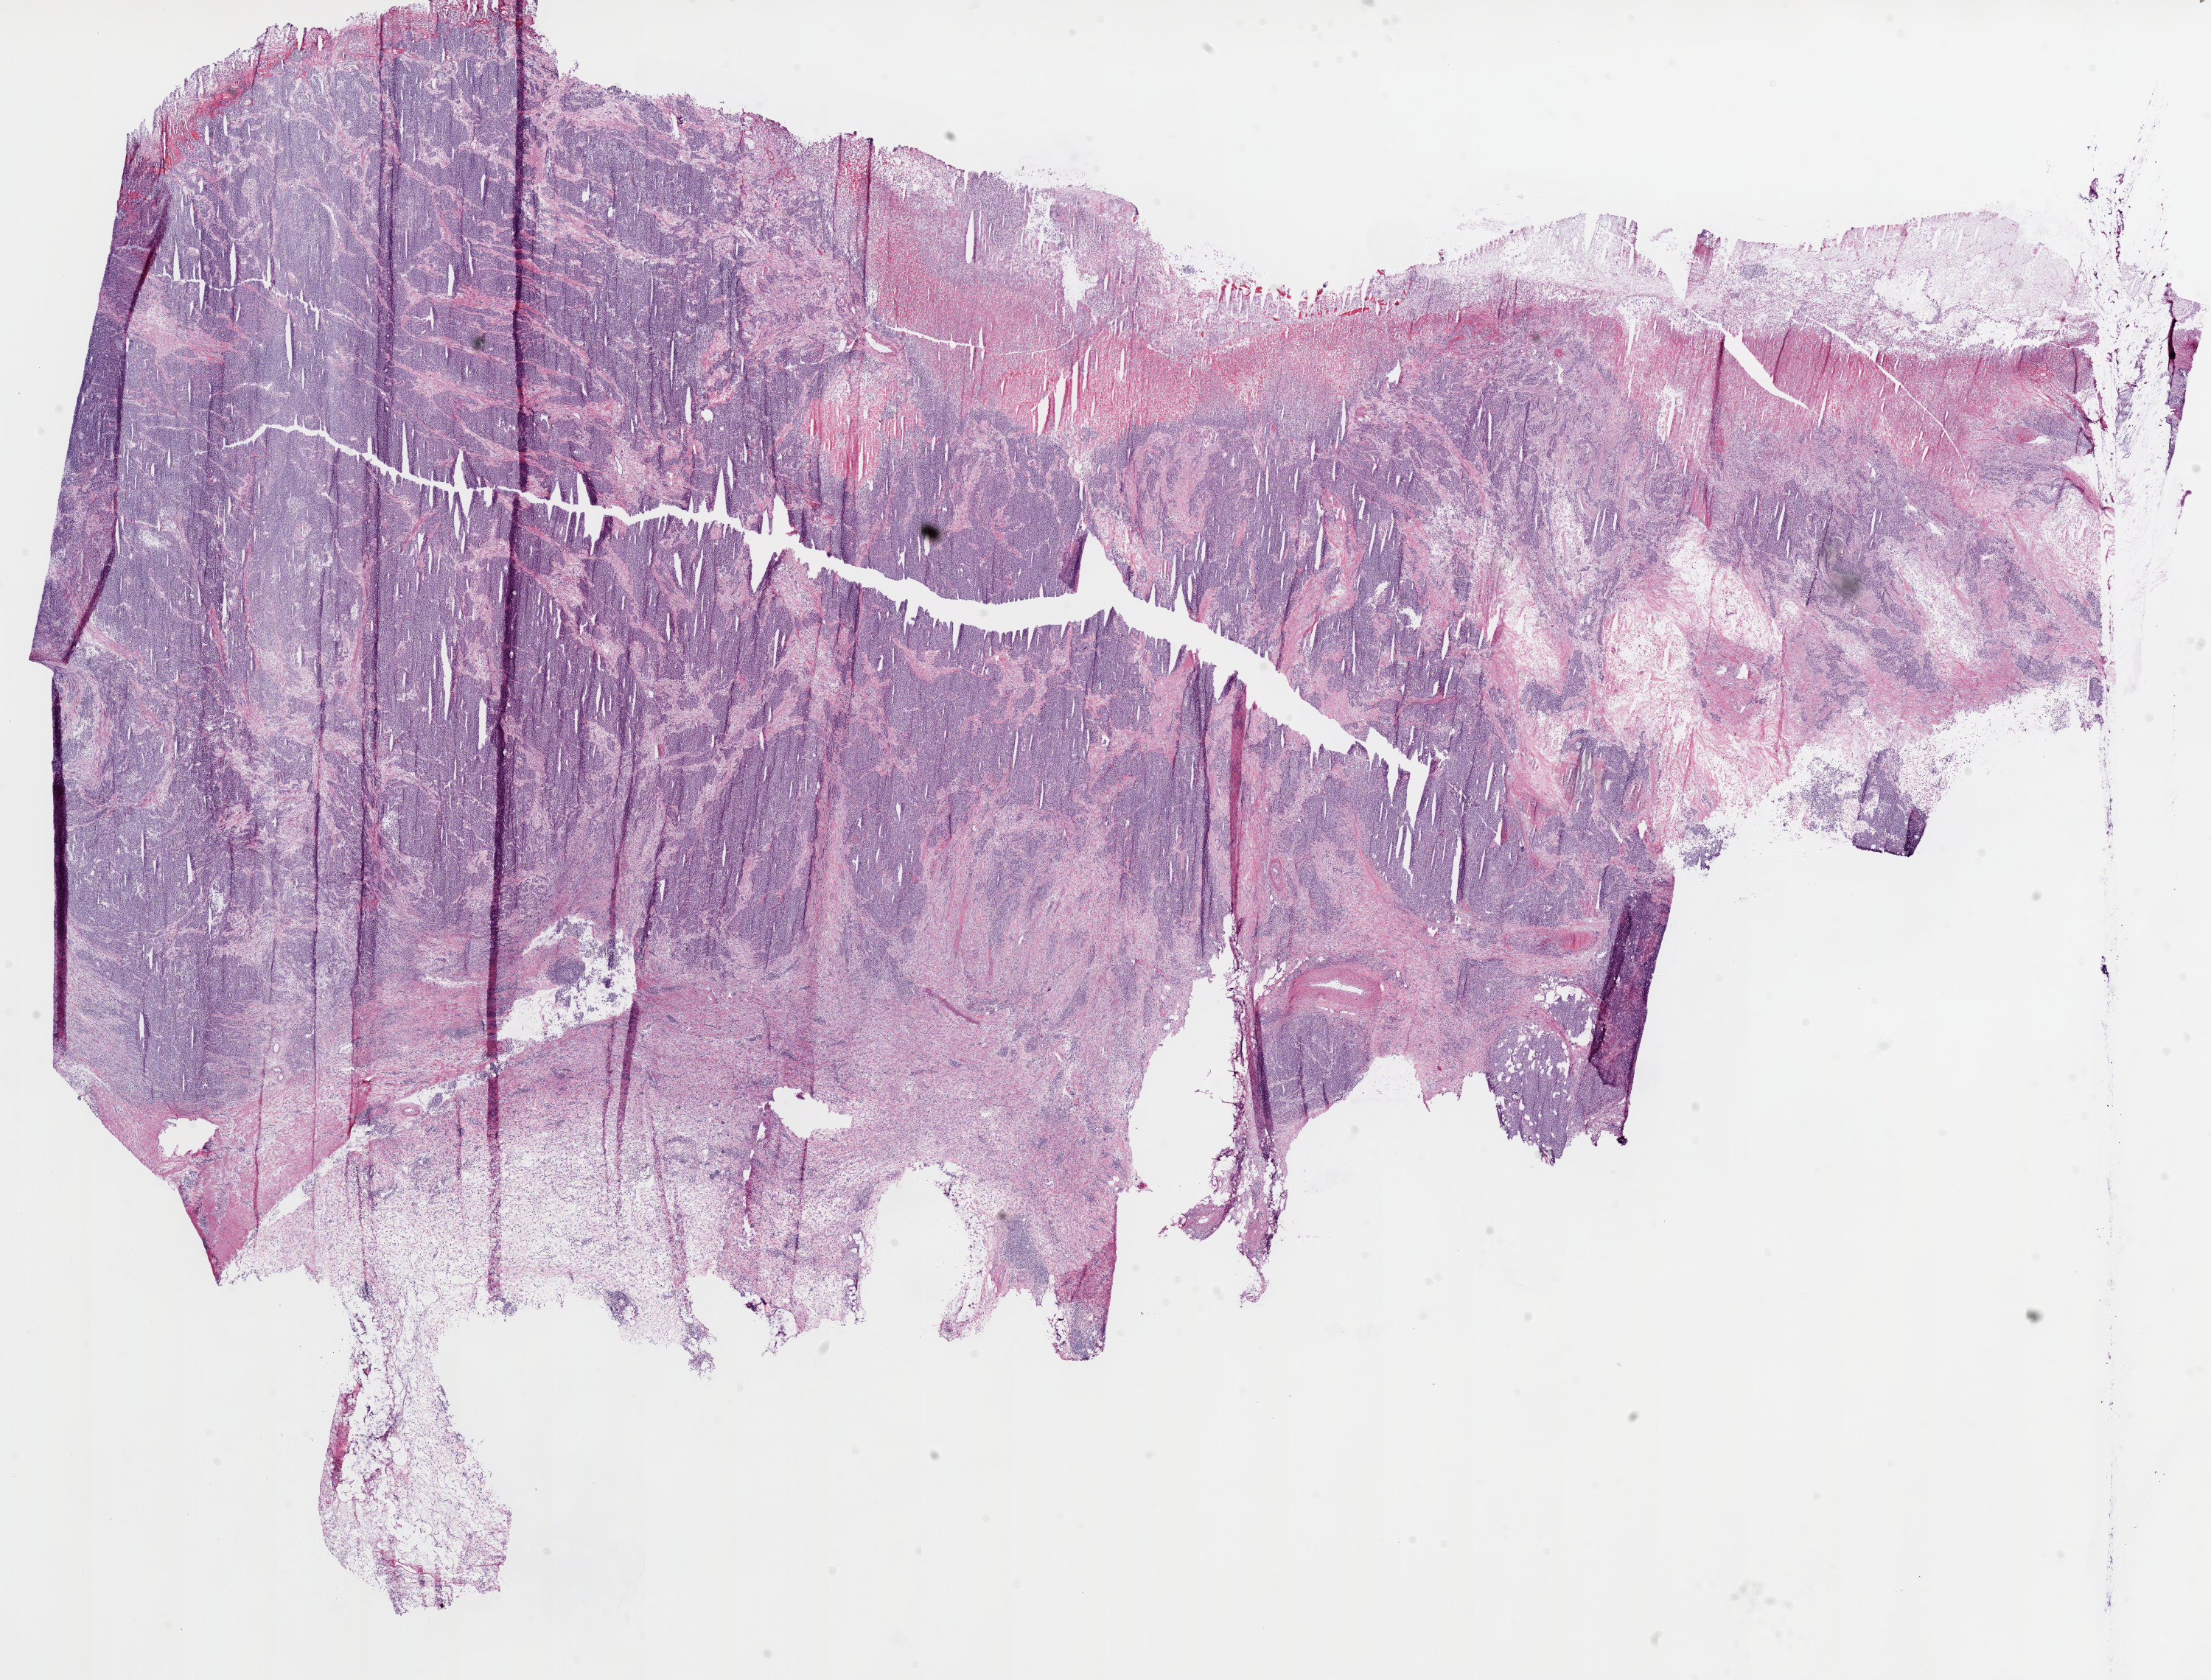
Whole-slide histology image, Hematoxylin and eosin (H&E) stained, a low-resolution overview of the entire scanned area, about 24.1 x 18.3 mm (slide scanned at 20x); frozen section; sample: primary tumour, stomach. Patient: female, age at initial diagnosis 60 years. Histologic grade: G3 (poorly differentiated). Composition of this section per pathologist review: tumour cells 70%, tumour nuclei 80%, normal cells 0%, stromal cells 20%, necrosis 10%.
- diagnosis: Adenocarcinoma, NOS (body of stomach)